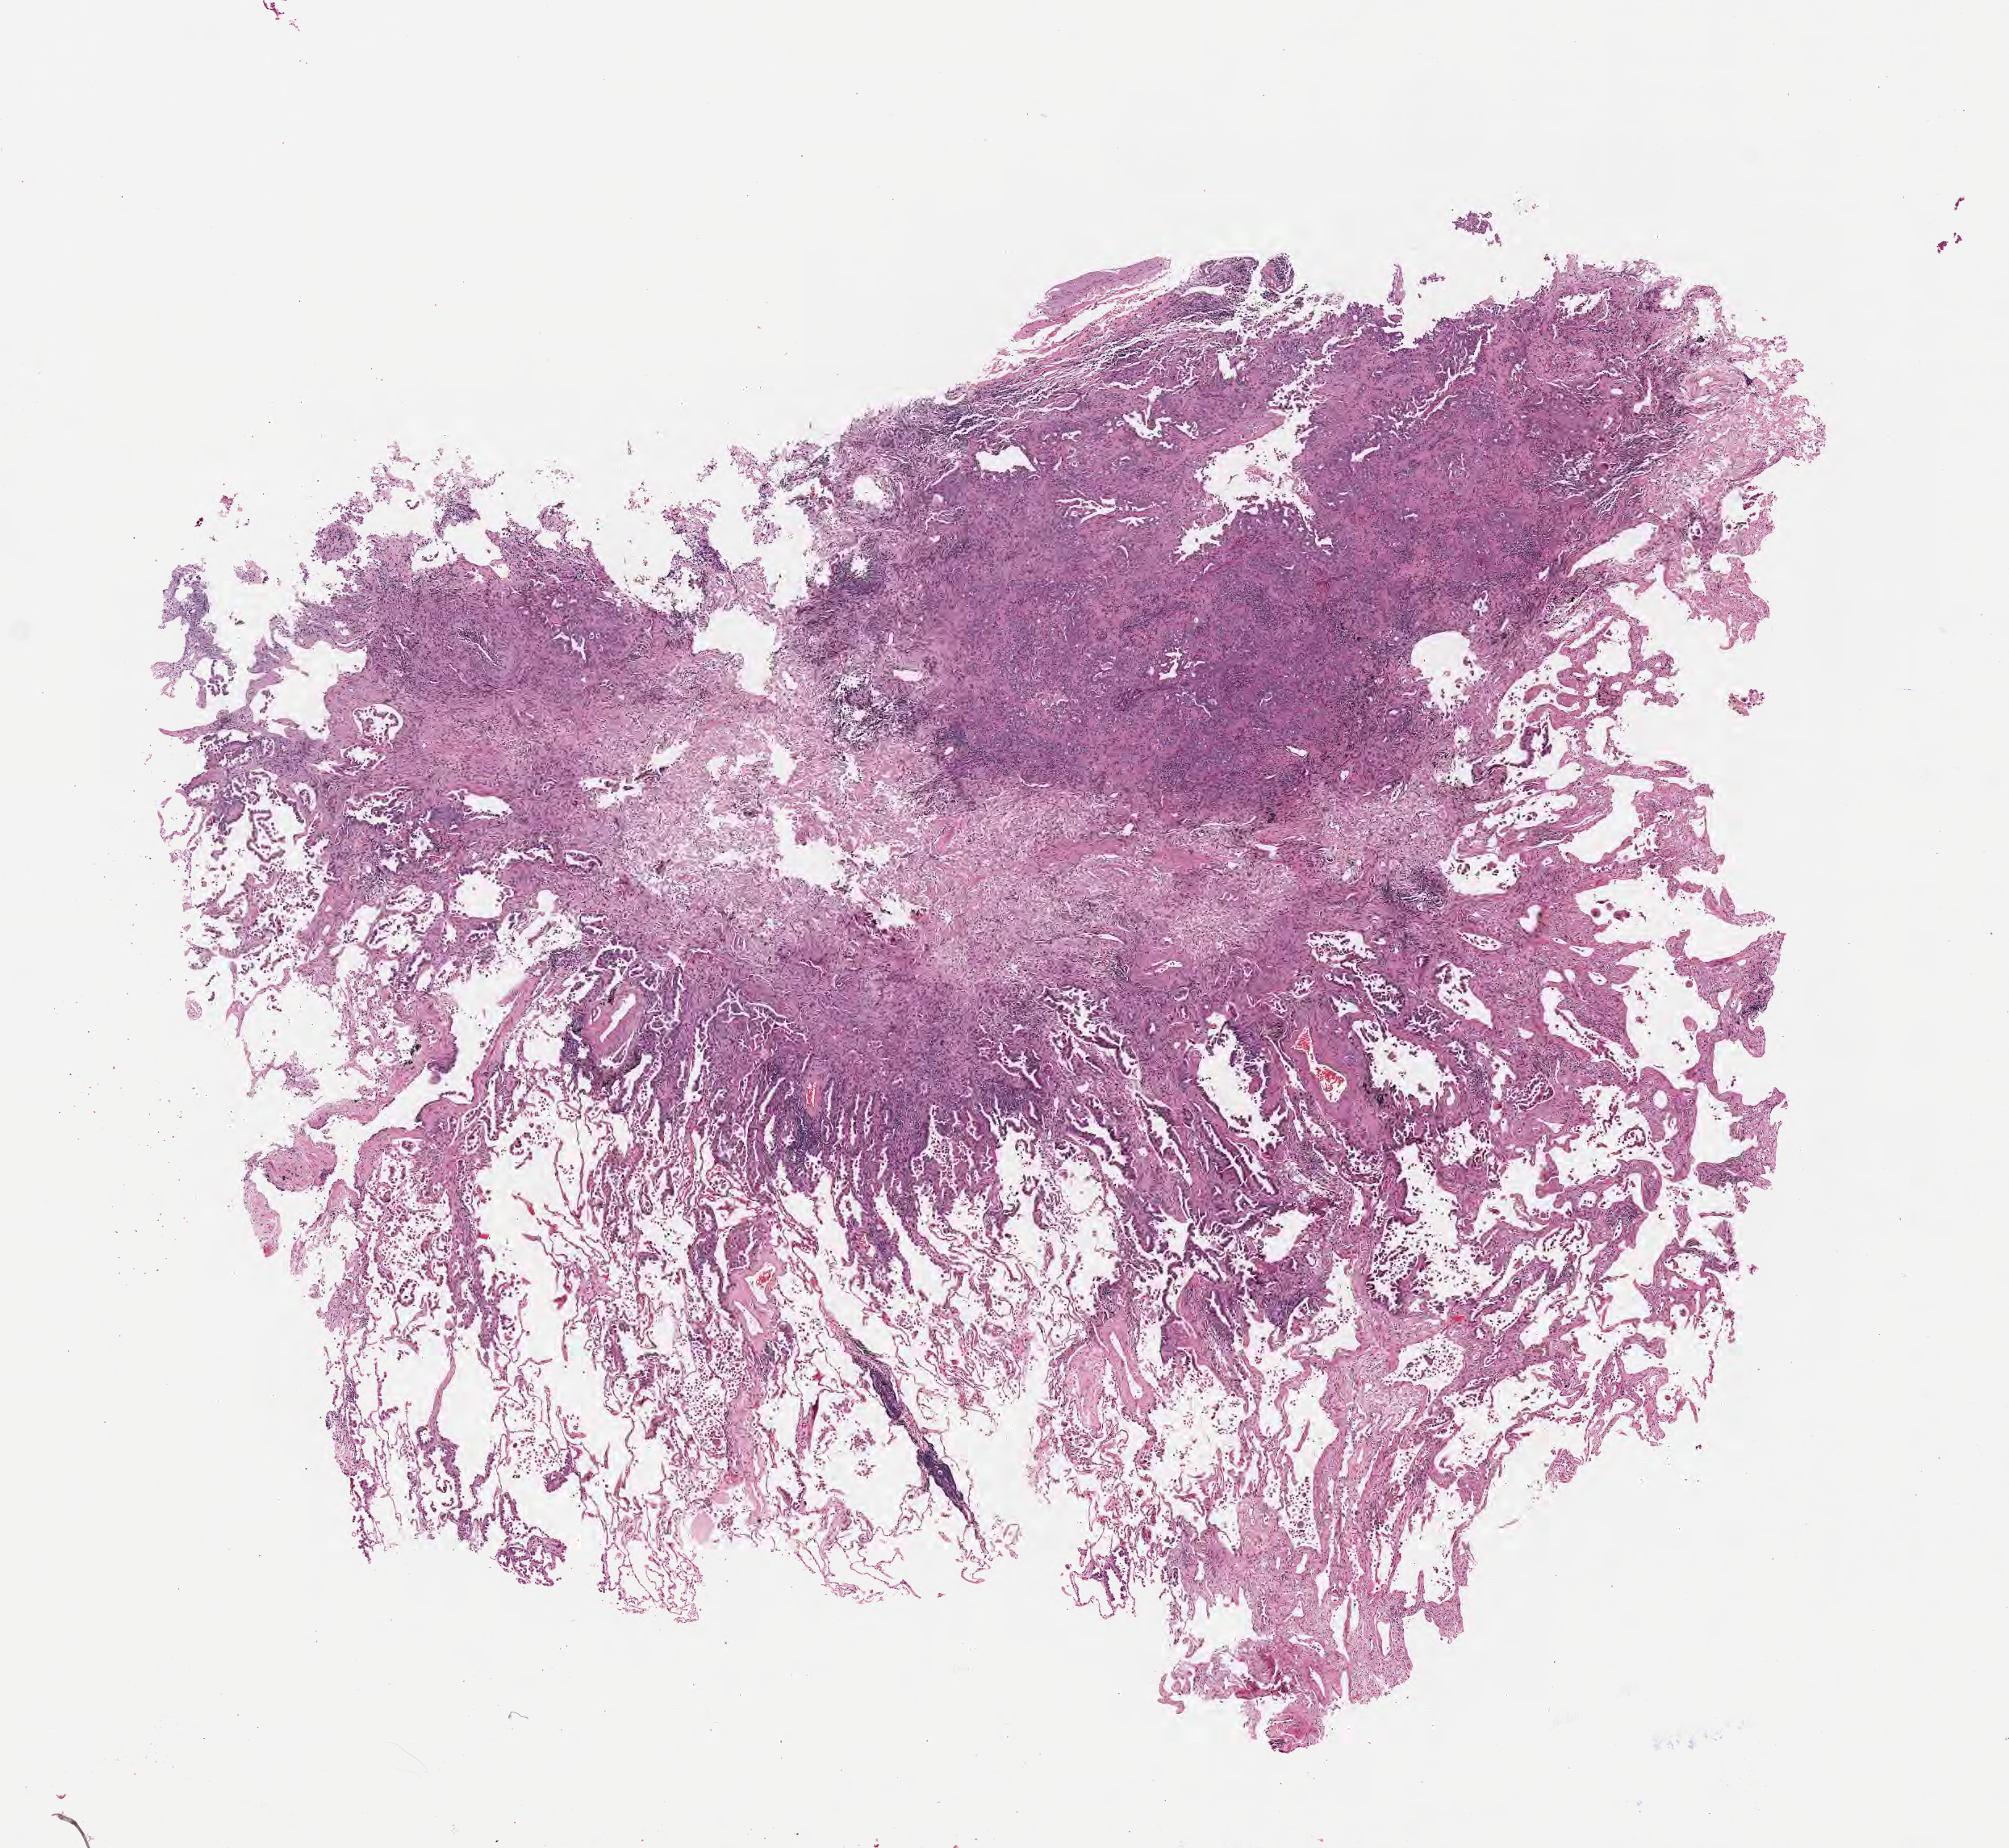
Digitized hematoxylin and eosin (H&E)-stained section — whole scanned area (about 10.1 x 9.3 mm) shown as a low-resolution overview; FFPE section; primary tumor; anatomic site: upper lobe of right lung. Male, age 82 years at initial diagnosis.
Histologic diagnosis: Adenocarcinoma, NOS.